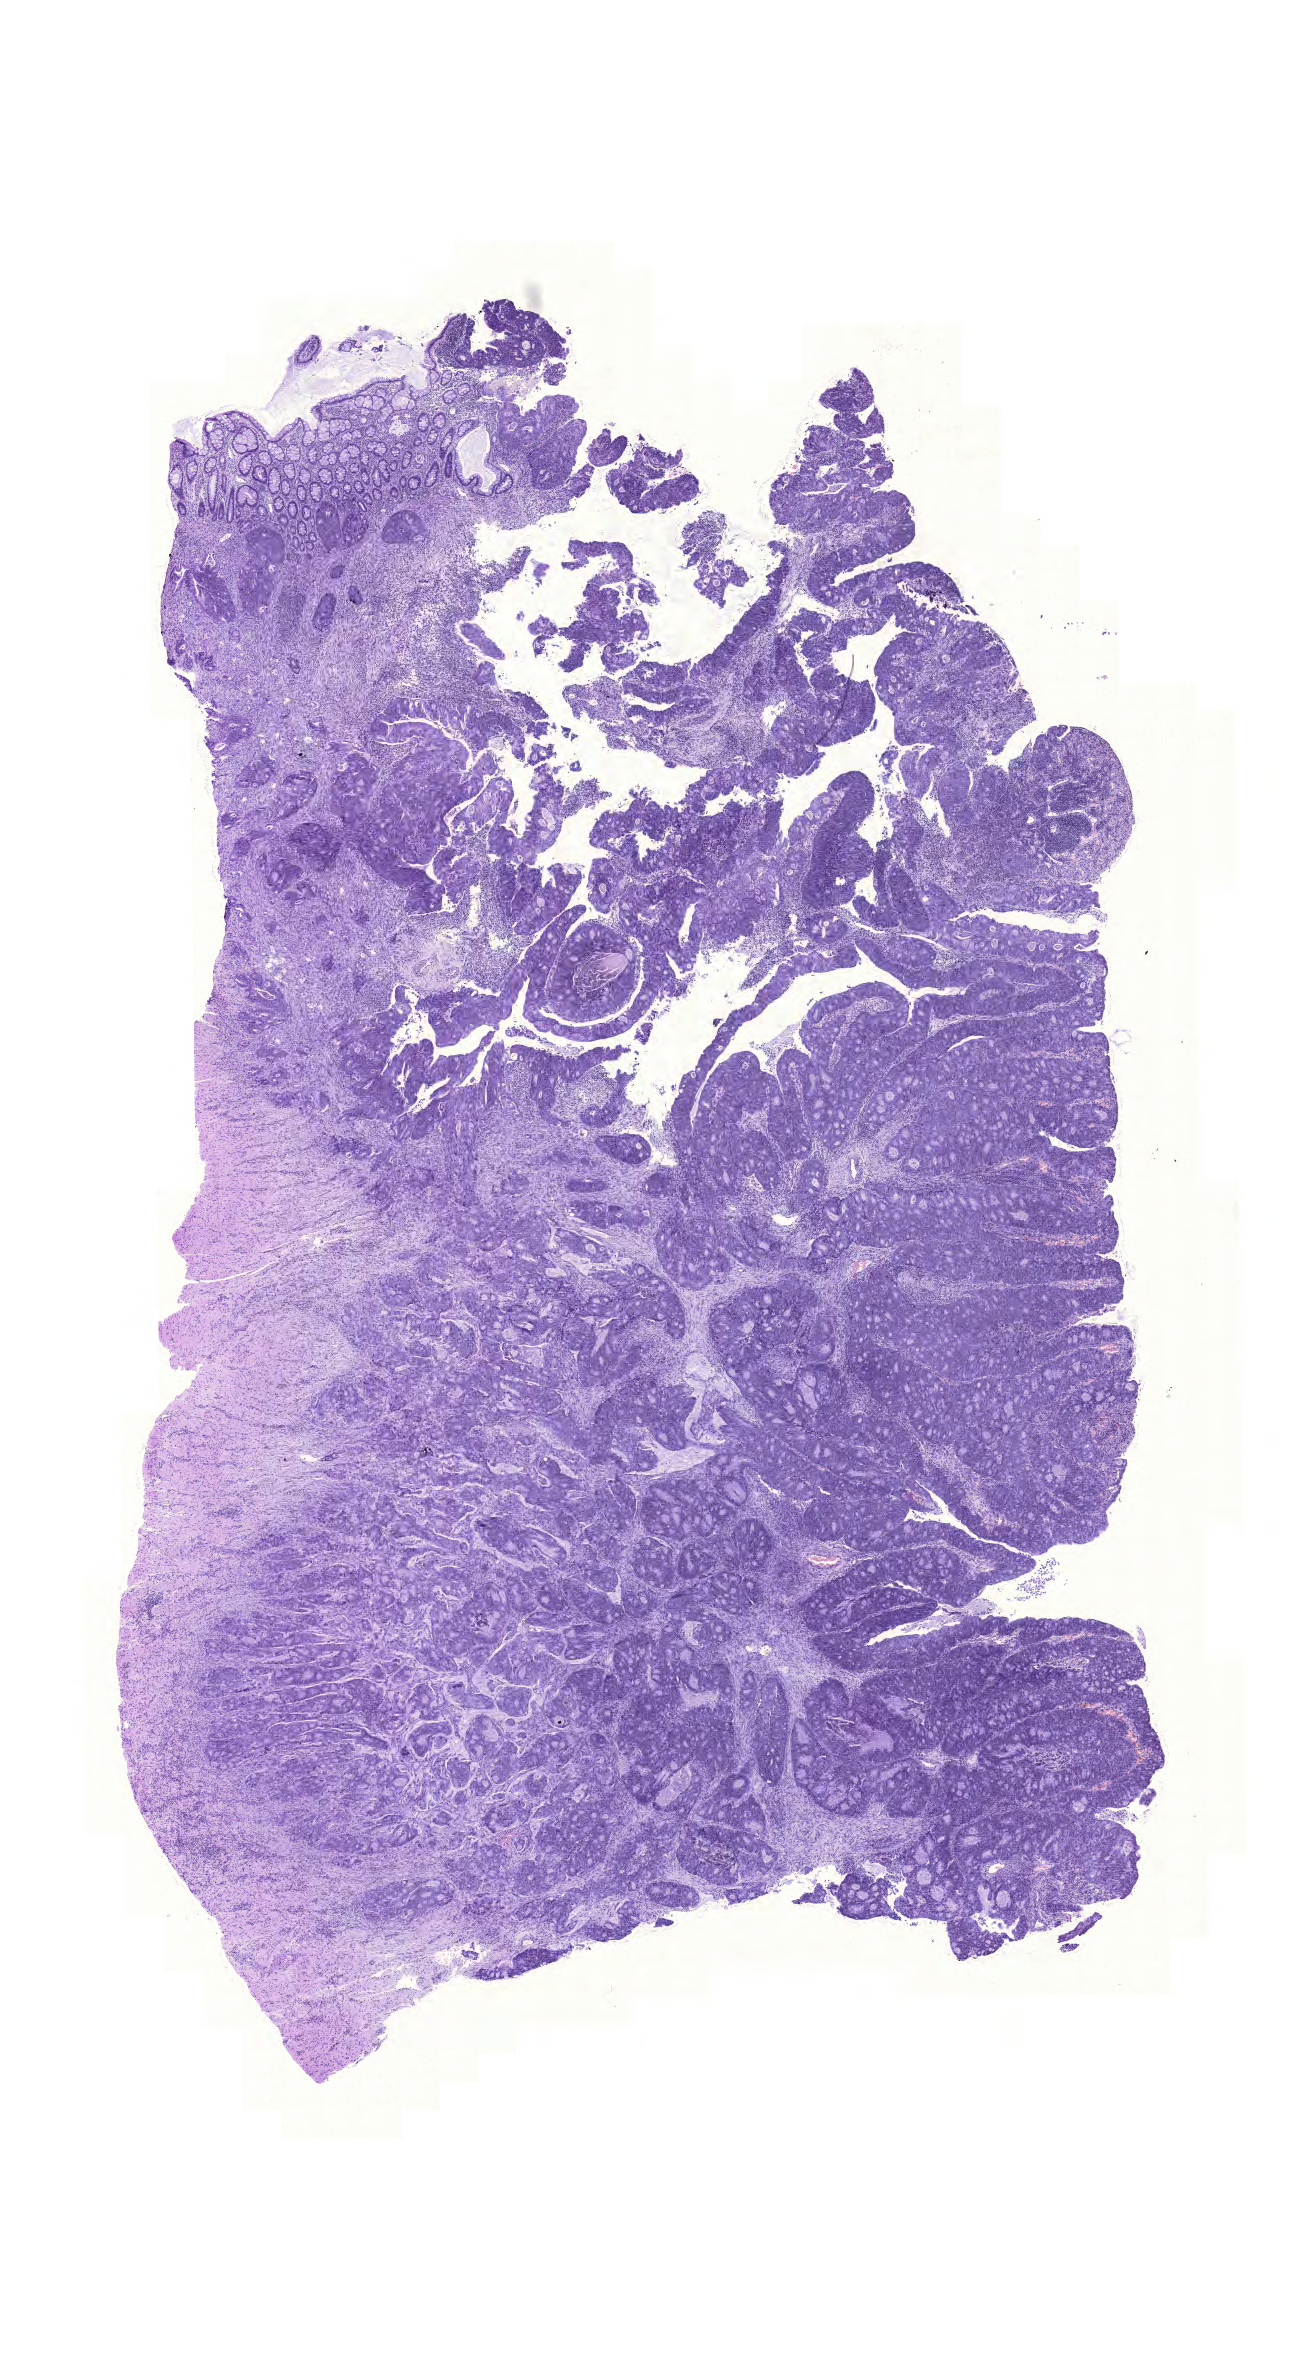
Hematoxylin and eosin (H&E) stained whole-slide image, whole scanned area (about 9.7 x 17.6 mm) shown as a low-resolution overview. Formalin-fixed paraffin-embedded (FFPE) diagnostic section. Rectum, primary tumour sample. Female patient; age at initial diagnosis 72 years.
Lymph nodes positive (case pathology): 4 of 19 examined. Pathologic diagnosis: Mucinous adenocarcinoma. AJCC pathologic stage: III (5th edition).